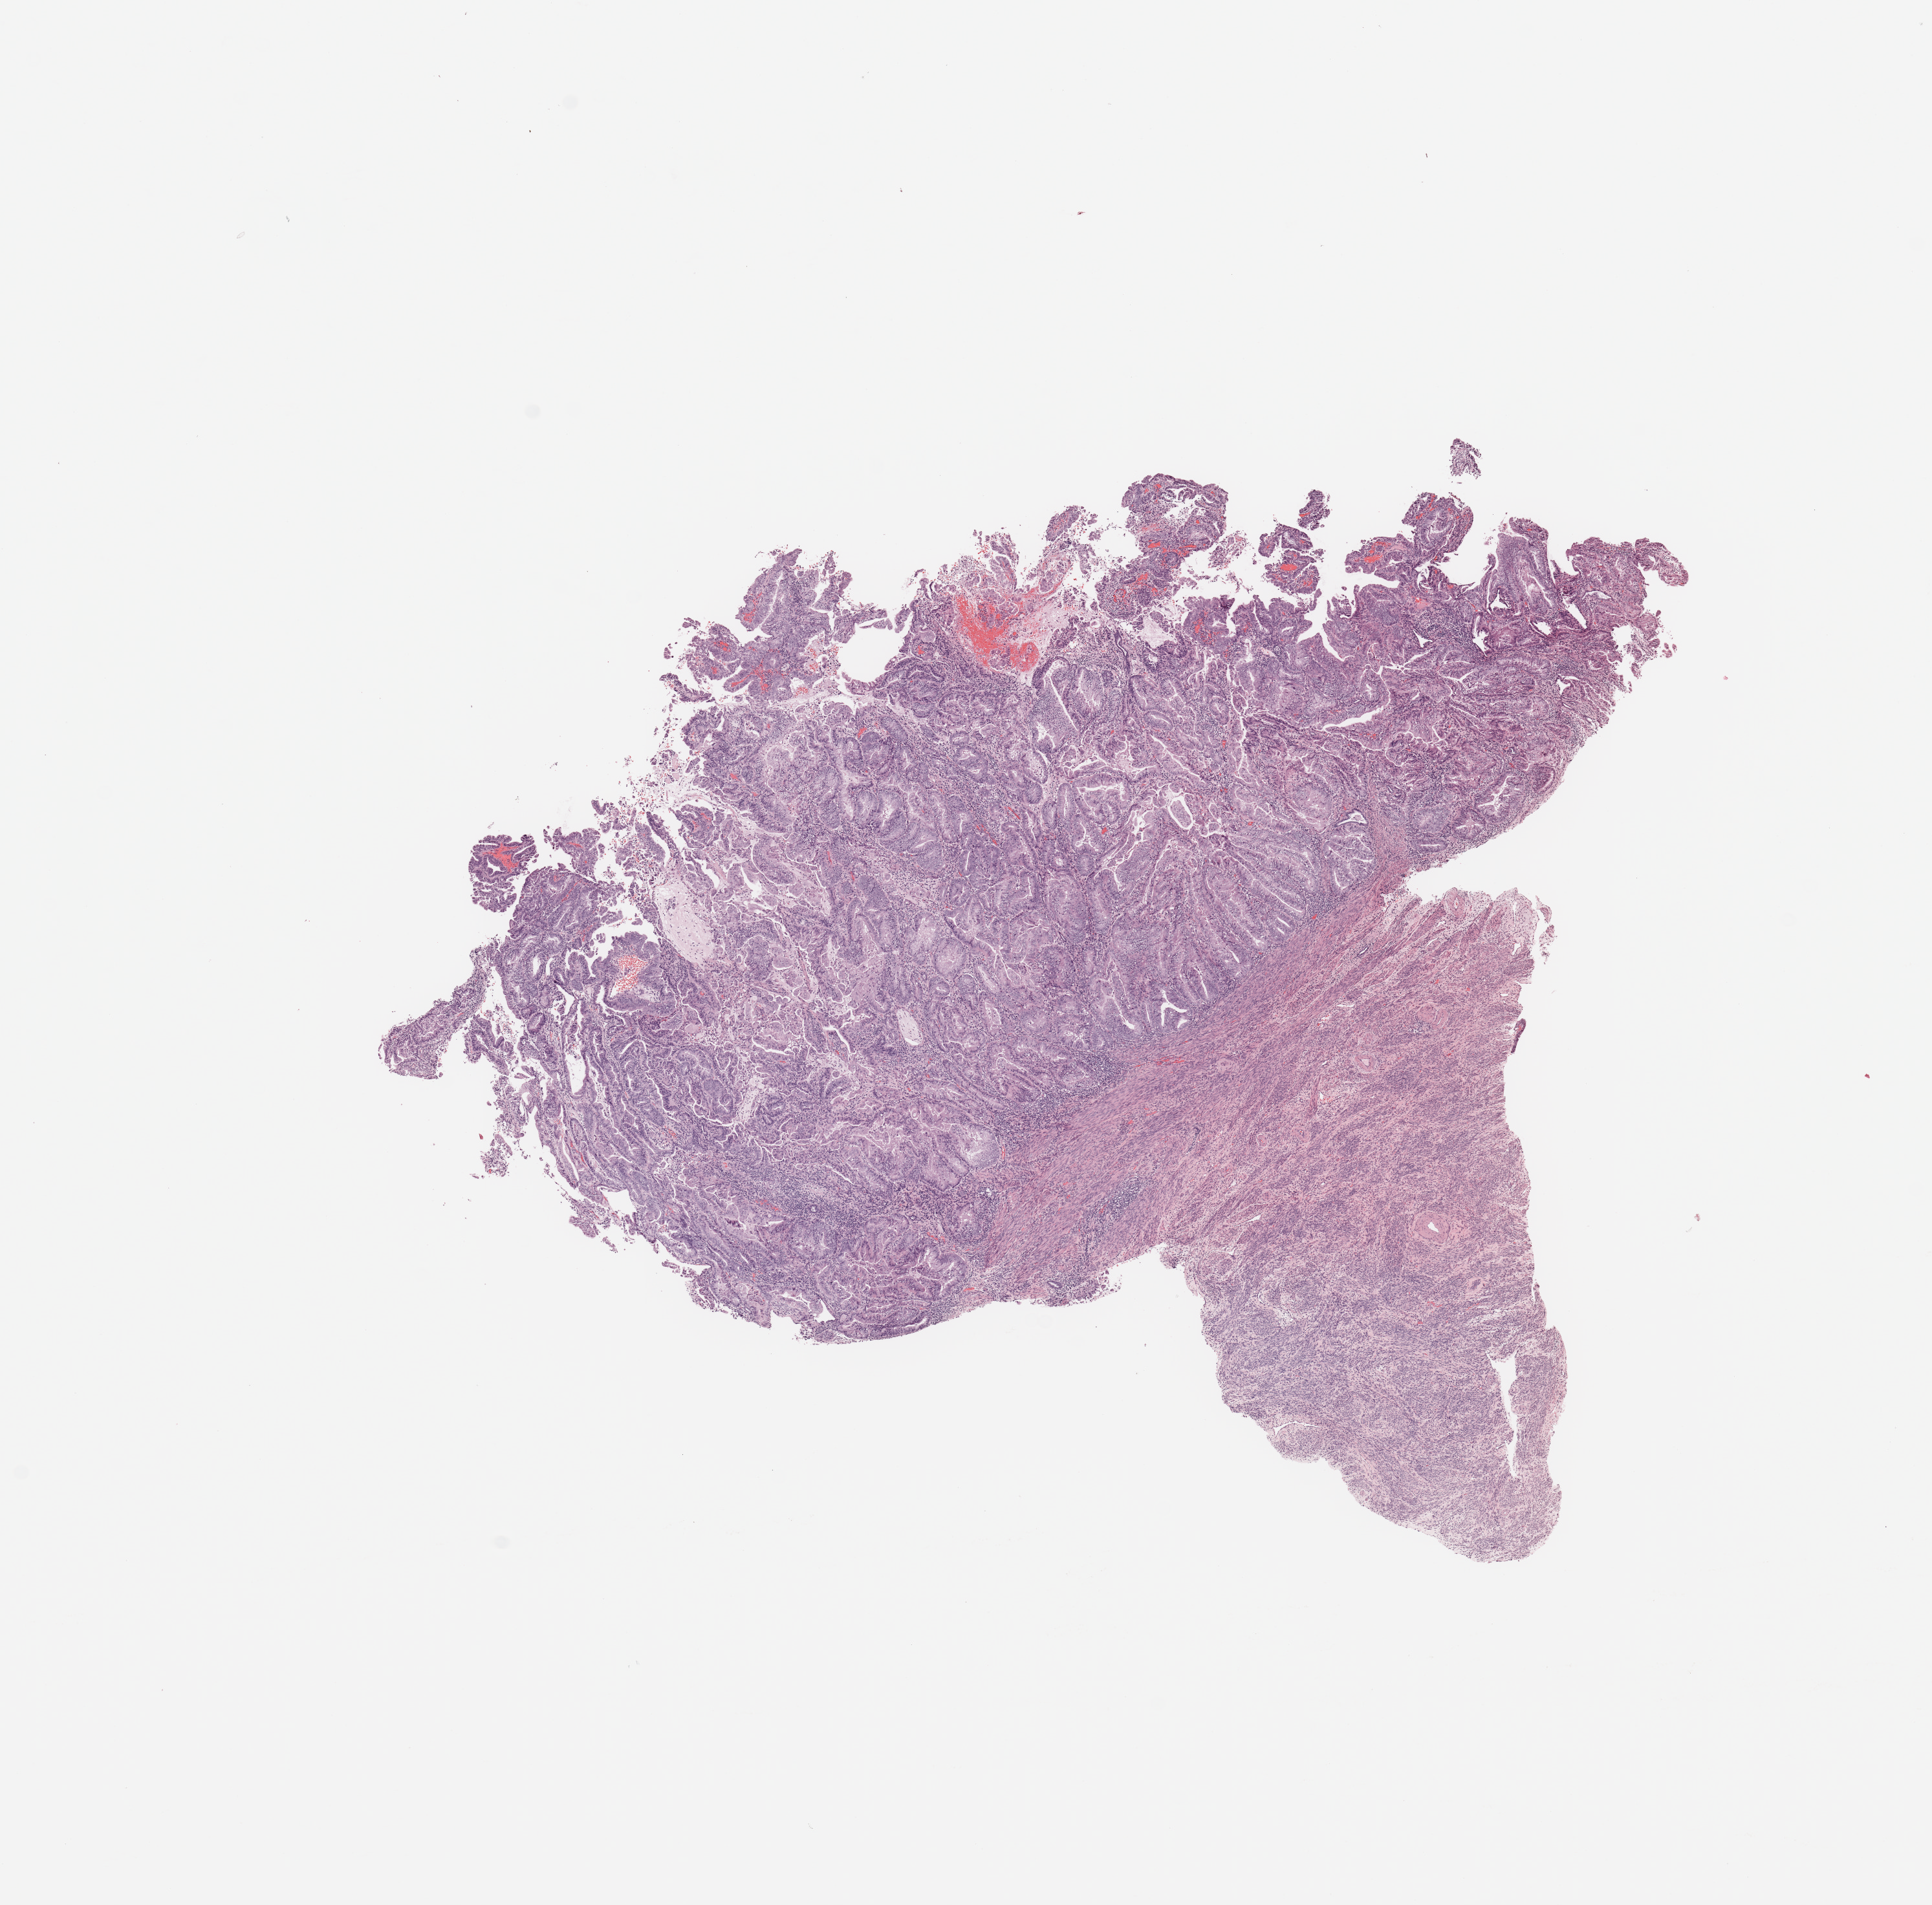
Digitized H&E tissue section (whole slide), a low-resolution overview of the entire scanned area, about 11.8 x 11.7 mm (slide scanned at 20x), tumour tissue sample, sampled site: uterus. Female, 60 y/o. Histologic grade: G2 (moderately differentiated). Pathologist review of this section (percent, as recorded): tumour nuclei 80%, necrosis 0%.
Diagnosis: Endometrioid adenocarcinoma, NOS. Primary tumour site (as recorded): posterior endometrium. AJCC pathologic stage: II.